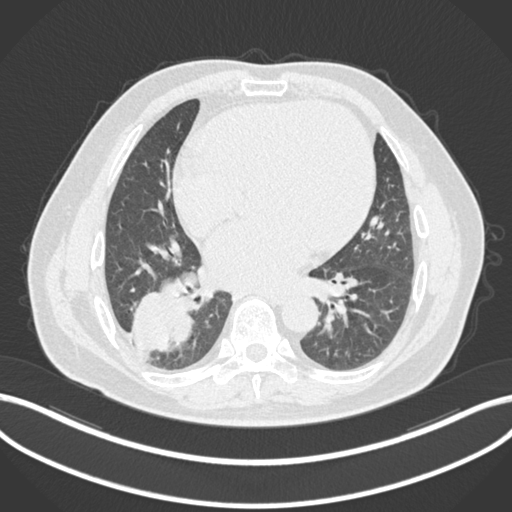
Chest CT, one axial slice; position 71 of 200 along the scan axis; reconstruction kernel B30f; 120 kVp; lung window (W 1500 / L -600 HU); 1 mm slice thickness; 512 × 512 image matrix, field of view 400 × 400 mm. Patient: male, 59 years.
Annotated regions visible in this slice (bounding box drawn by a radiologist):
- lung tumour (recorded histology: adenocarcinoma): box from (x=130, y=286) to (x=196, y=358) px